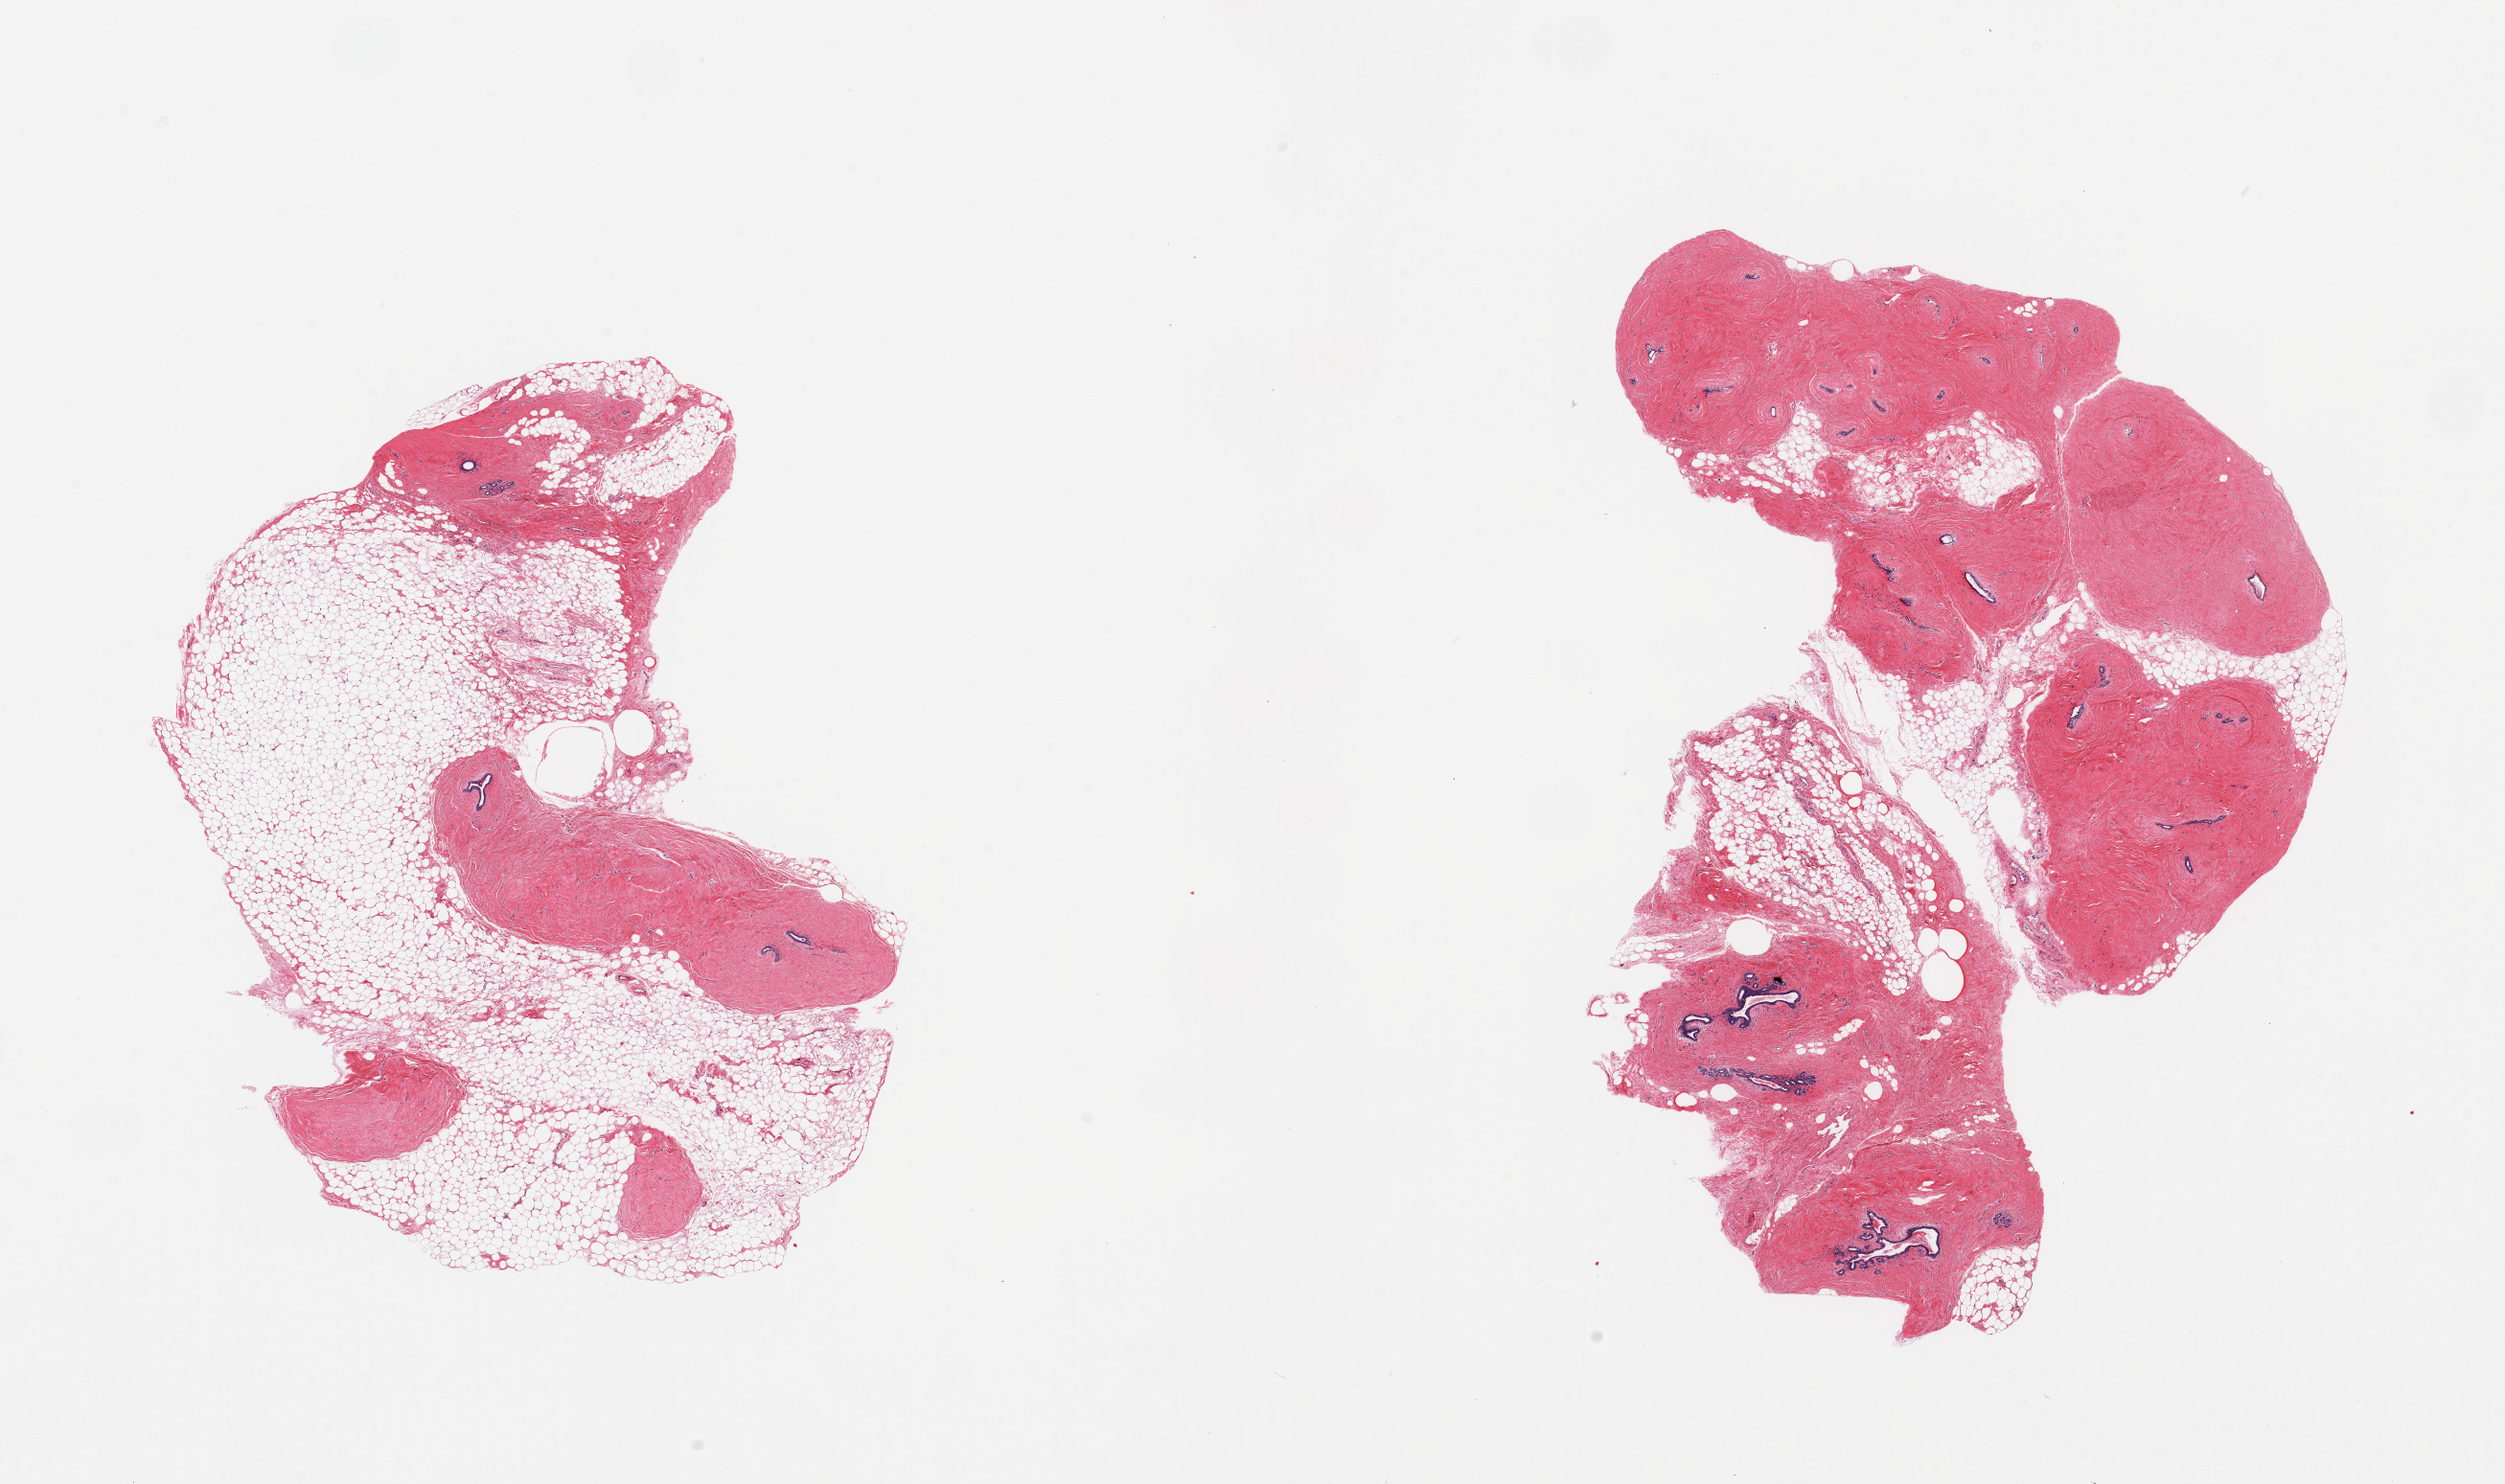
Haematoxylin and eosin whole-slide image — whole scanned area (about 20.7 x 12.3 mm, slide scanned at 20x) shown as a low-resolution overview; PAXgene-fixed paraffin-embedded (PFPE) section; target tissue: breast; tissue donor sample. Donor: female.
Reviewer comment on this tissue sample: 2 pieces; atrophic ducts and lobules.